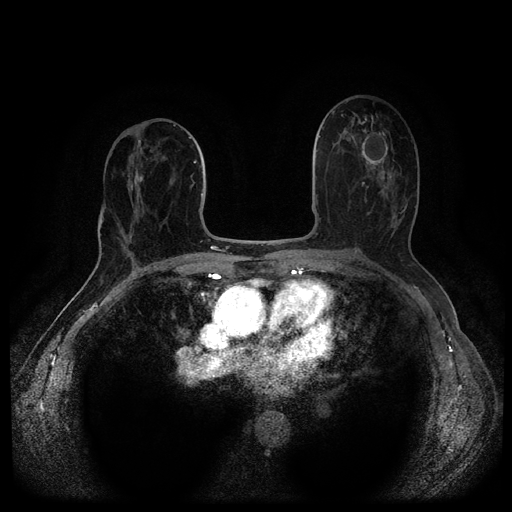
Breast MRI (dynamic contrast-enhanced, multi-phase), one axial slice; slice 54 of 116 in the series (ordered by position); dynamic contrast-enhanced series, time point 2 of 5 at this slice position (early post-contrast); 1.5 T; TE 2.6 ms, TR 5.4 ms; 512 × 512 image matrix, field of view 340 × 340 mm. Female patient, age 69 years.
Structures marked on this image (semi-automatic segmentation, software-assisted and operator-edited):
- breast lesion (labelled benign in the annotation): box from (x=358, y=131) to (x=389, y=169) px